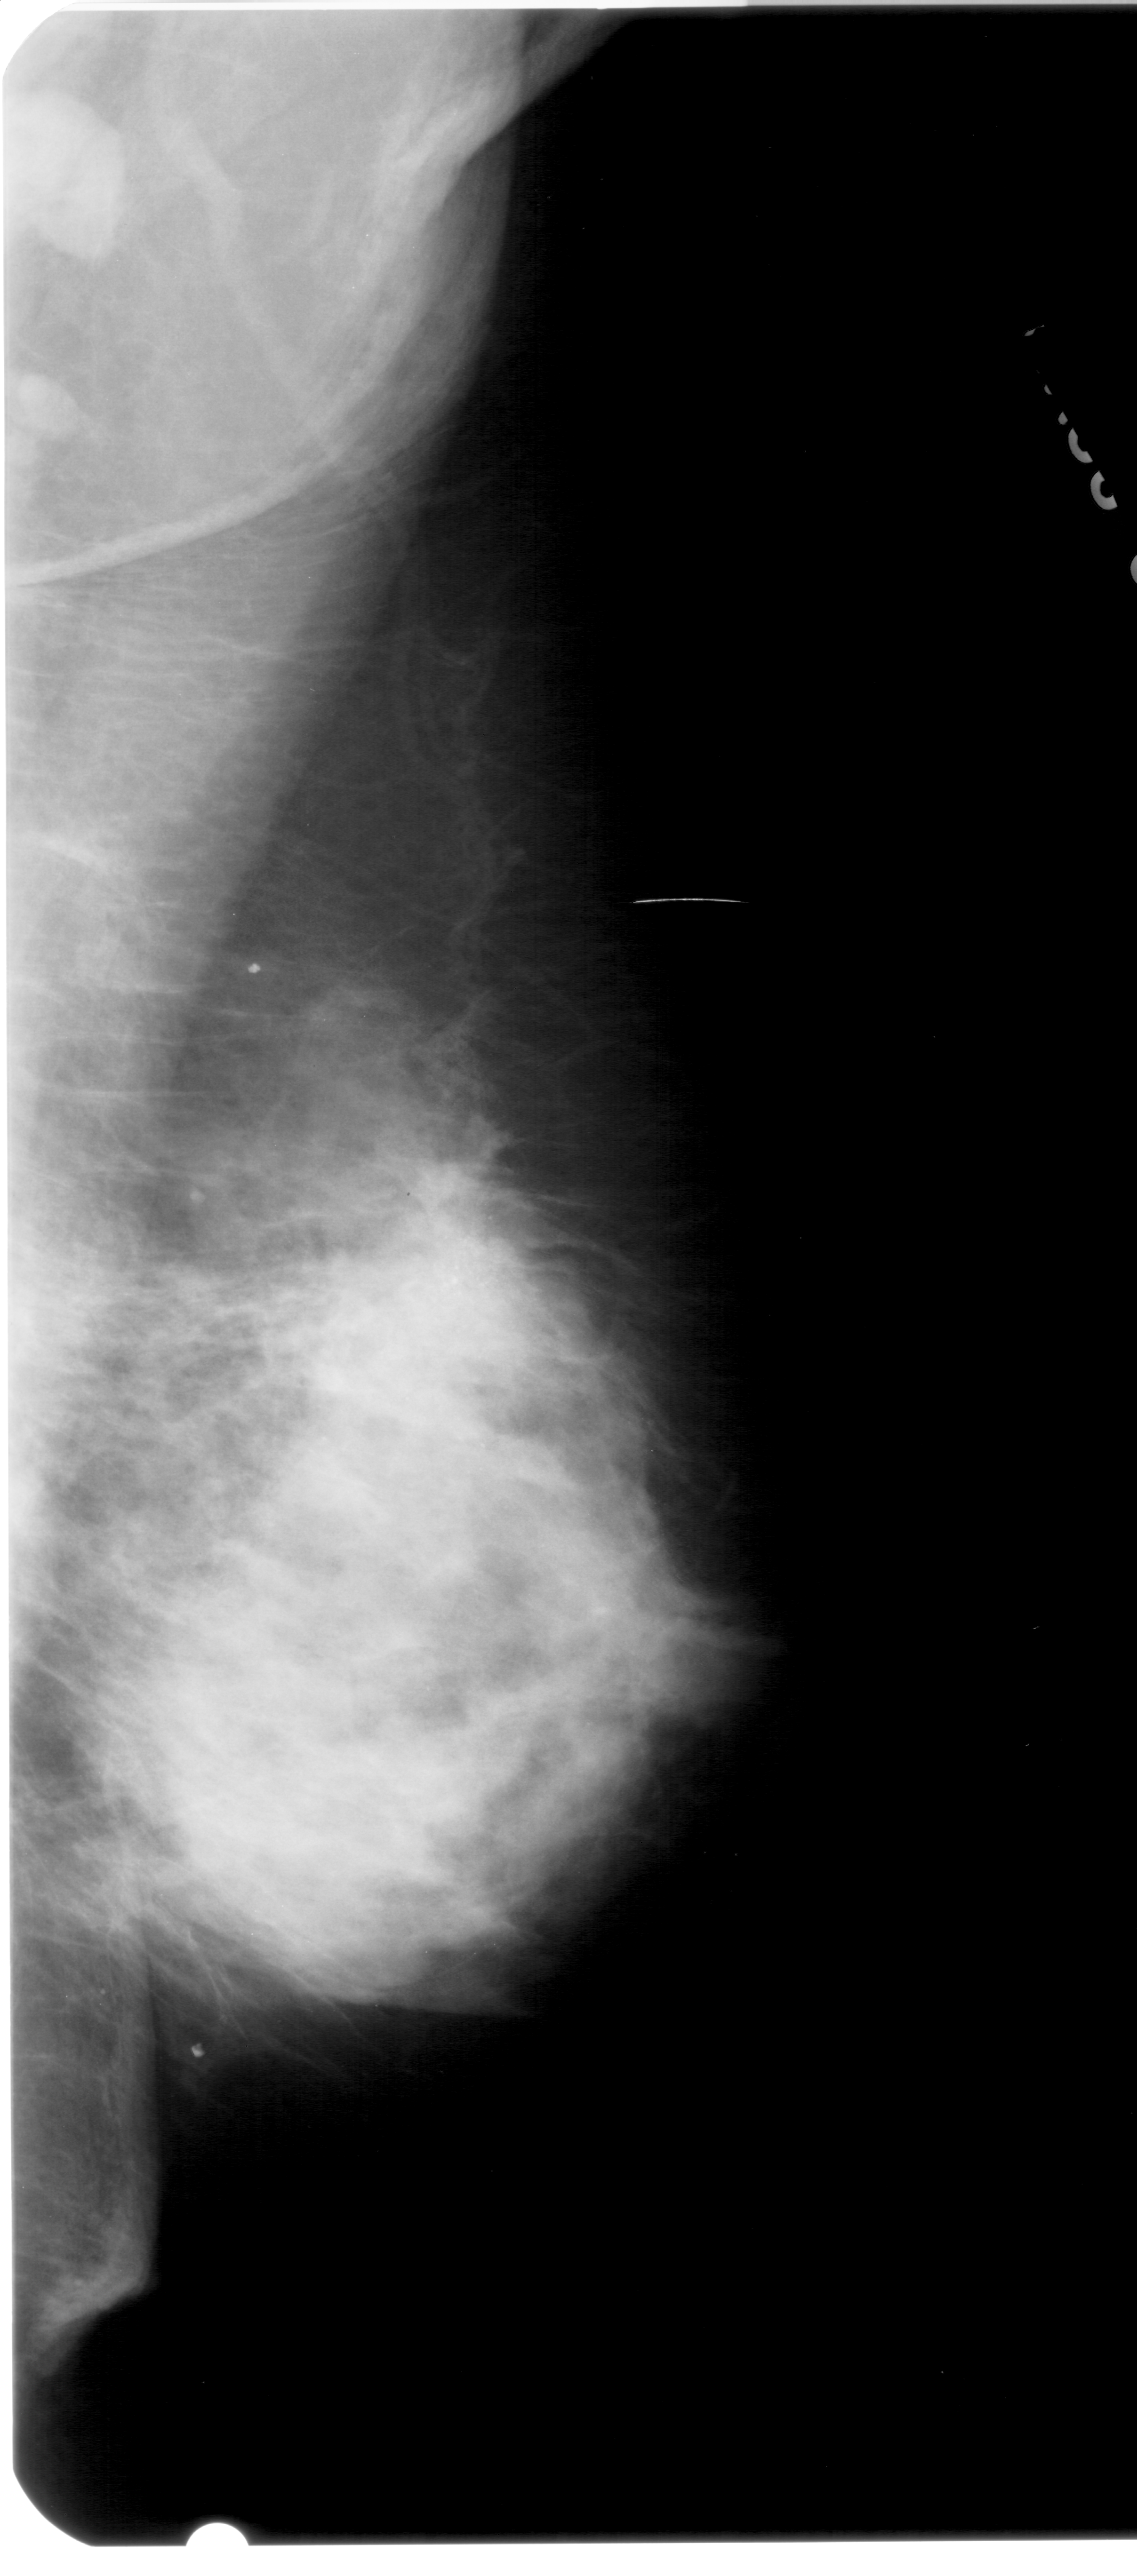
Mammogram (digitized film); right breast; MLO view; breast composition: heterogeneously dense (BI-RADS density category 3 of 4); 1137 × 2576 image matrix.
Expert-marked regions of interest on this film, with their recorded descriptors:
- mass, shape architectural distortion, margins spiculated; BI-RADS assessment category 5; pathology result (as recorded, not read from the image): malignant: bounding box [x1, y1, x2, y2] px = [422, 1228, 523, 1310]